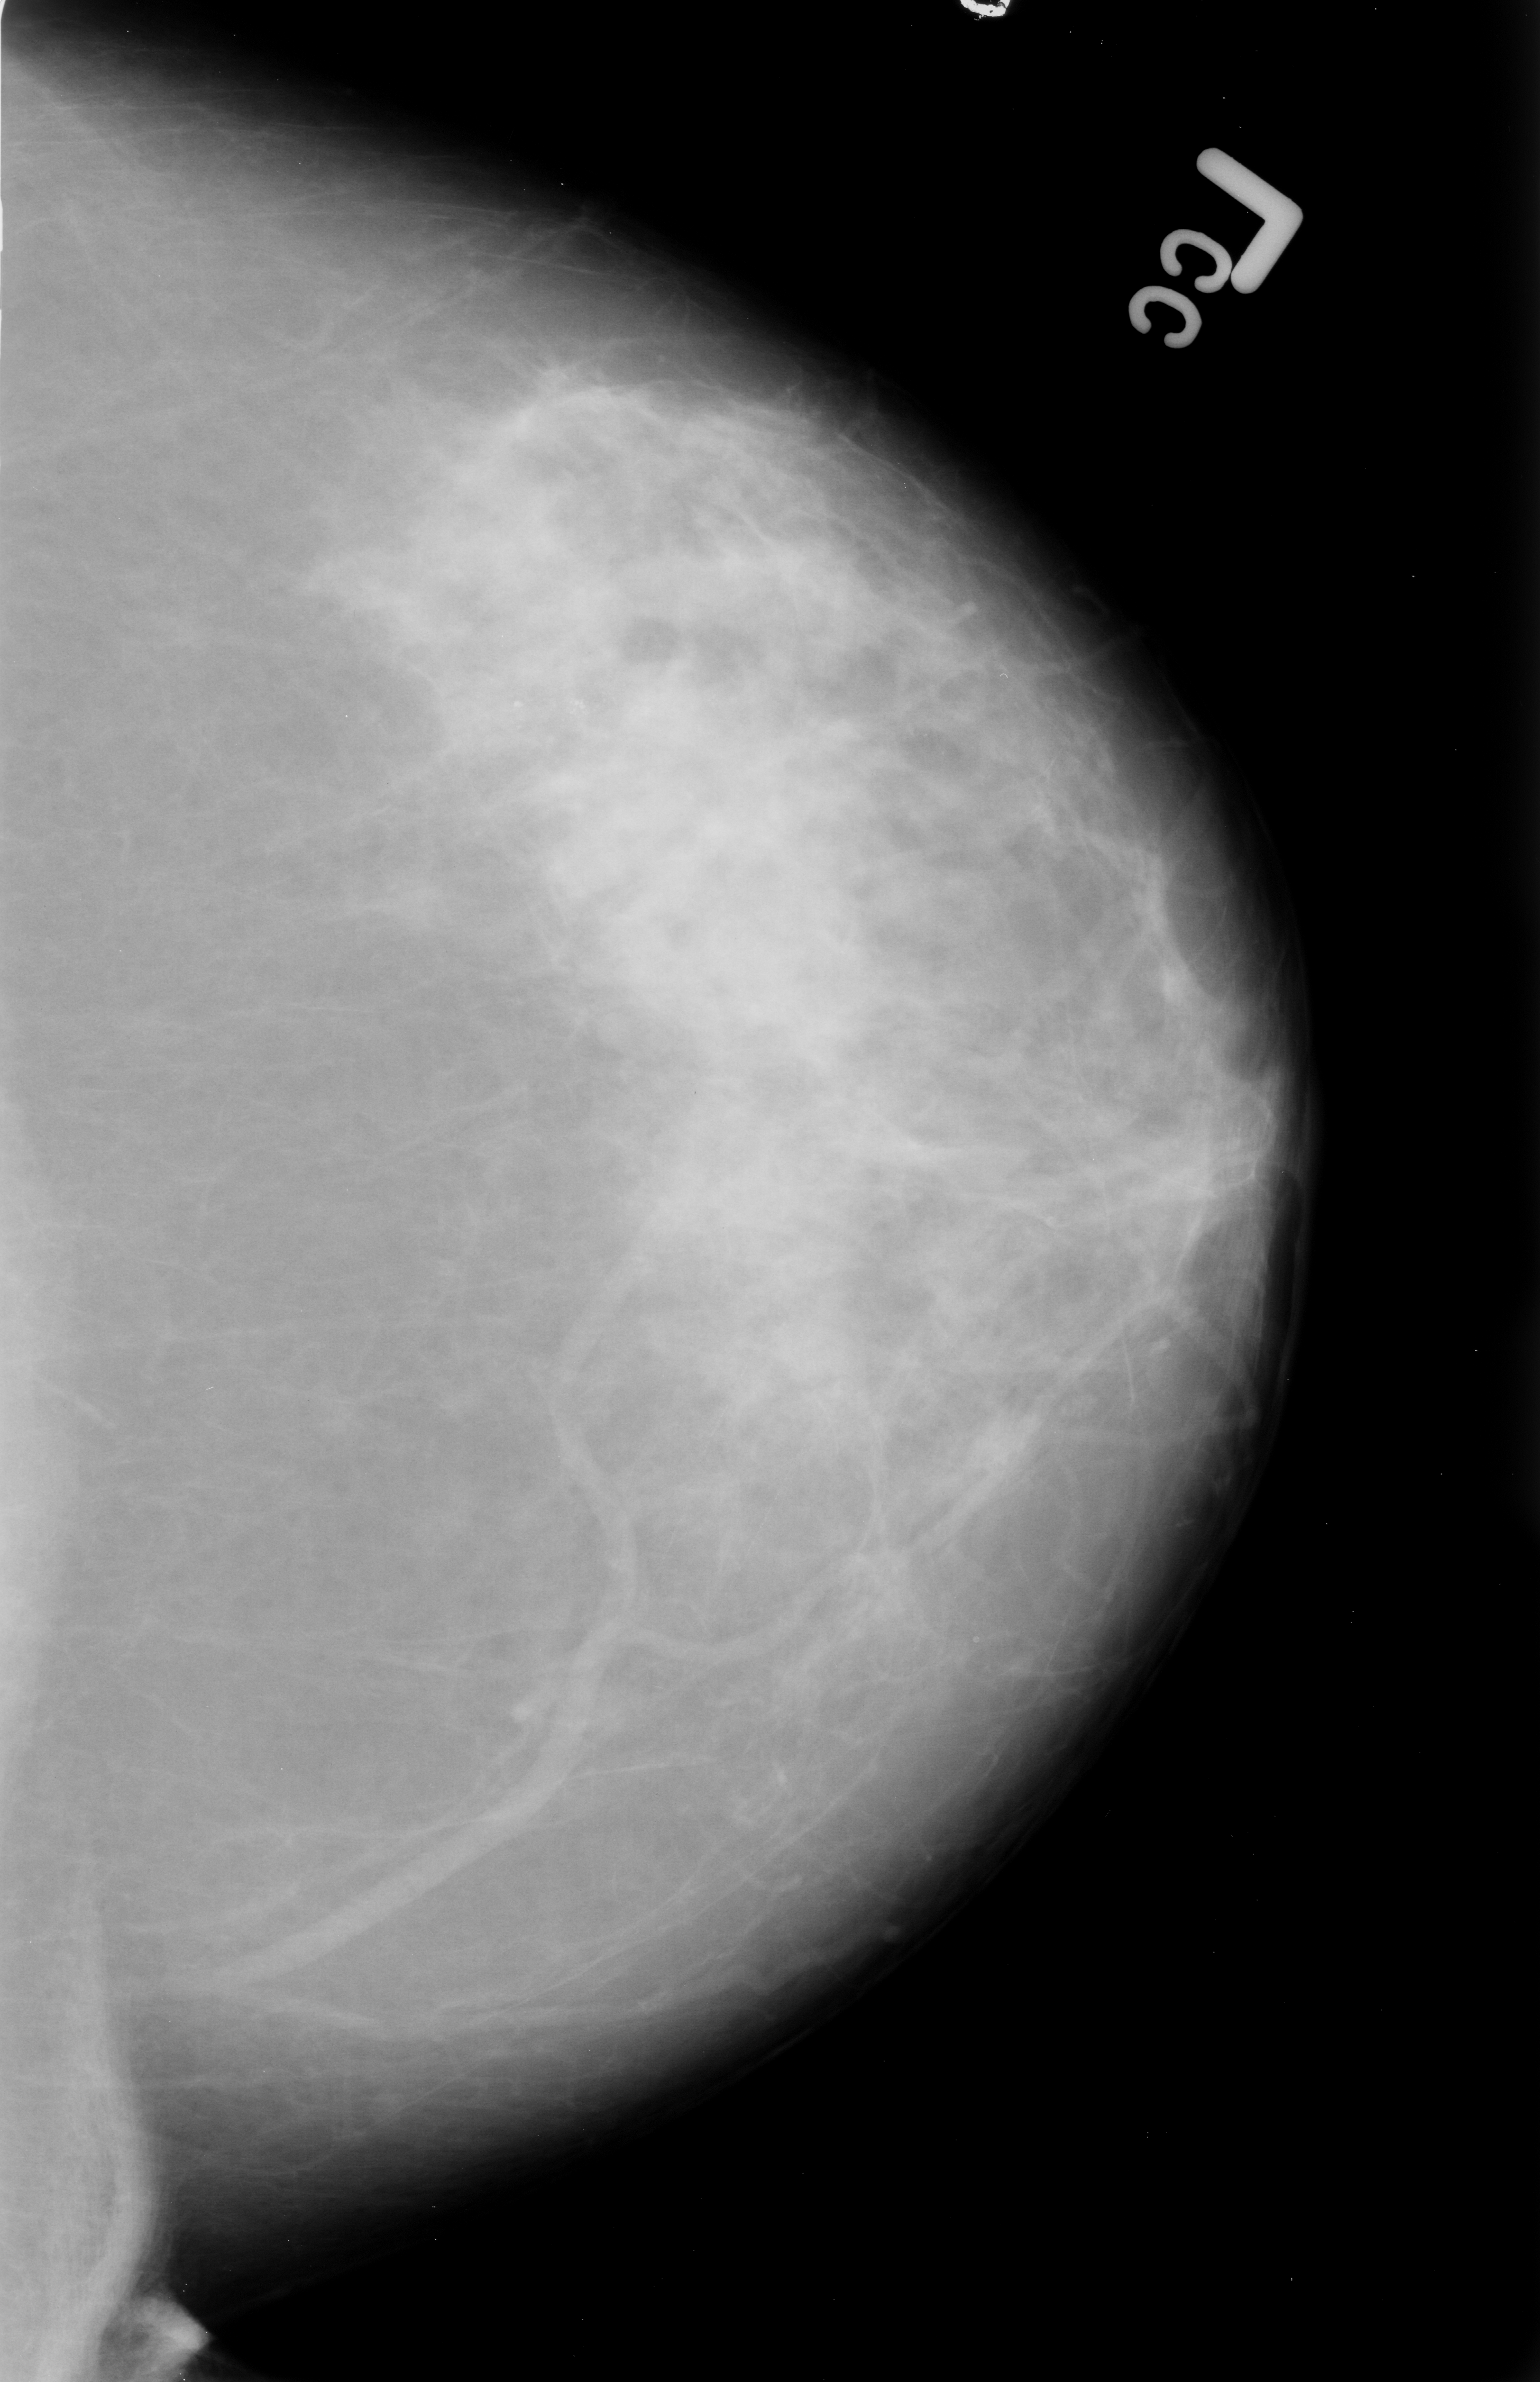
Digitized screen-film mammogram. Left breast. CC view. Breast composition: scattered fibroglandular densities (BI-RADS density category 2 of 4). 1540 × 2382 image matrix.
Expert-marked regions of interest on this film, with their recorded descriptors:
- calcifications, morphology pleomorphic, distribution clustered; BI-RADS assessment category 4; pathology result (as recorded, not read from the image): malignant: bounding box [x1, y1, x2, y2] px = [444, 655, 610, 767]